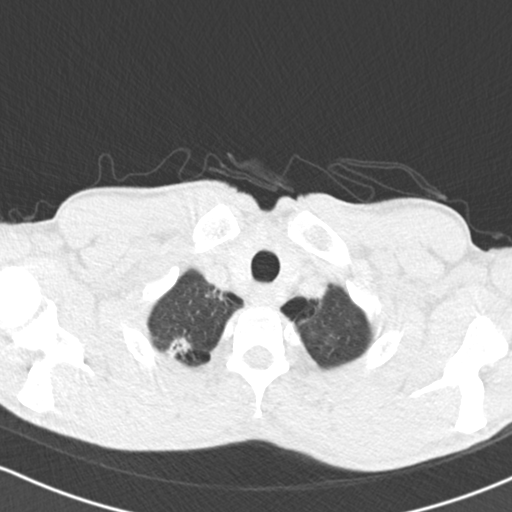
Low-dose screening chest CT, one axial slice. Position 129 of 150 along the scan axis. Reconstruction kernel B30f. Lung window (W 1500 / L -600 HU). 2 mm slice thickness. 512 × 512 image matrix, field of view 312 × 312 mm.
Annotated regions visible in this slice (outlined manually by an expert reader):
- lesion 1 (tumor, upper lobe of right lung): bounding box [x1, y1, x2, y2] px = [166, 337, 191, 360]